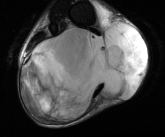
MRI of an extremity soft-tissue mass, one axial slice. T2-weighted fat-saturated. MR volume resampled by the dataset authors to the PET/CT grid (not the native acquisition matrix). 3.27 mm slice thickness. 165 × 137 image matrix, field of view 161 × 134 mm. Male patient. From the clinical record (not read from this slice): histological type: liposarcoma - round cell; grade: high; site of the primary tumour: right calf.
Outlined on this slice (expert contour drawn on MRI and transferred to this co-registered scan by the dataset authors):
- gross tumour volume (mass): bounding box (x1, y1, x2, y2) in pixels: (21, 20, 149, 120)